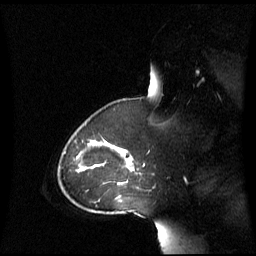
Breast MRI (dynamic contrast-enhanced), one sagittal slice; slice 45 of 60 in the series (ordered by position); dynamic contrast-enhanced series, image 2 of 3 at this slice position (ordered by acquisition); 1.5 T; TE 4.2 ms, TR 8.4 ms; 256 × 256 image matrix. Patient: female, 43 years. From the clinical record (not read from this slice): setting: breast cancer imaged before/during neoadjuvant chemotherapy; receptor status: triple-negative.
Structures marked on this image (semi-automatic segmentation, software-assisted and operator-edited):
- analysis volume of interest (the breast-tissue region the enhancement analysis was run in; not a lesion): bounding box <69,137,138,198> (left, top, right, bottom; pixels)
- tumour enhancement mask (voxels above the 70 % enhancement threshold inside the analysis volume of interest): <116,149,131,172>